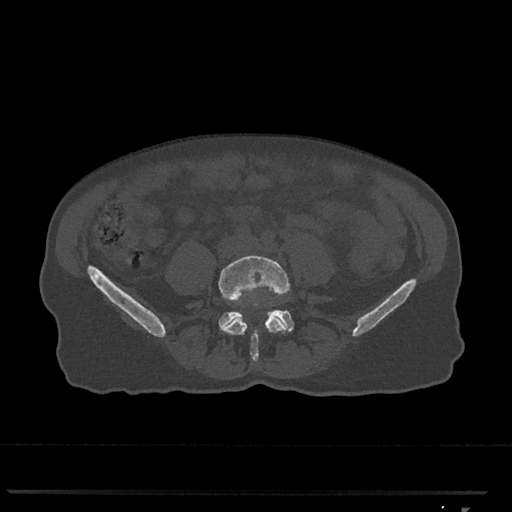
CT including the spine, one axial slice; slice 184 of 793 in the series (ordered by position); reconstruction kernel Br40s/3; bone window (W 1800 / L 400 HU); 0.5 mm slice thickness; 512 × 512 image matrix, field of view 380 × 380 mm. Female patient, age 62 years. Case-level facts recorded for this patient, not image findings: primary cancer: renal.
Structures marked on this image (semi-automatically segmented with operator editing):
- L4 vertebra: box from (x=219, y=255) to (x=290, y=362) px
- L5 vertebra: (x=219, y=310)–(x=294, y=331)